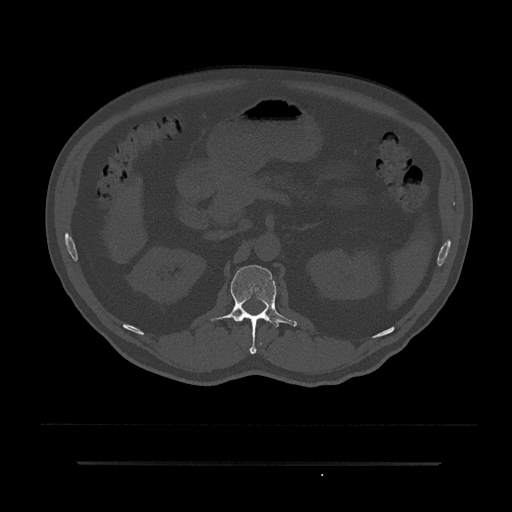
CT including the spine, one axial slice; slice 148 of 797 in the series (ordered by position); reconstruction kernel Br40s/3; 120 kVp; bone window (W 1800 / L 400 HU); 512 × 512 image matrix, field of view 464 × 464 mm. Patient: male, 59 years. Case-level facts recorded for this patient, not image findings: primary cancer: bile ducts; vertebrae with lytic lesions (as recorded): T10.
Outlined on this slice (semi-automatically segmented with operator editing):
- L1 vertebra: bounding box [x1, y1, x2, y2] px = [211, 265, 298, 354]